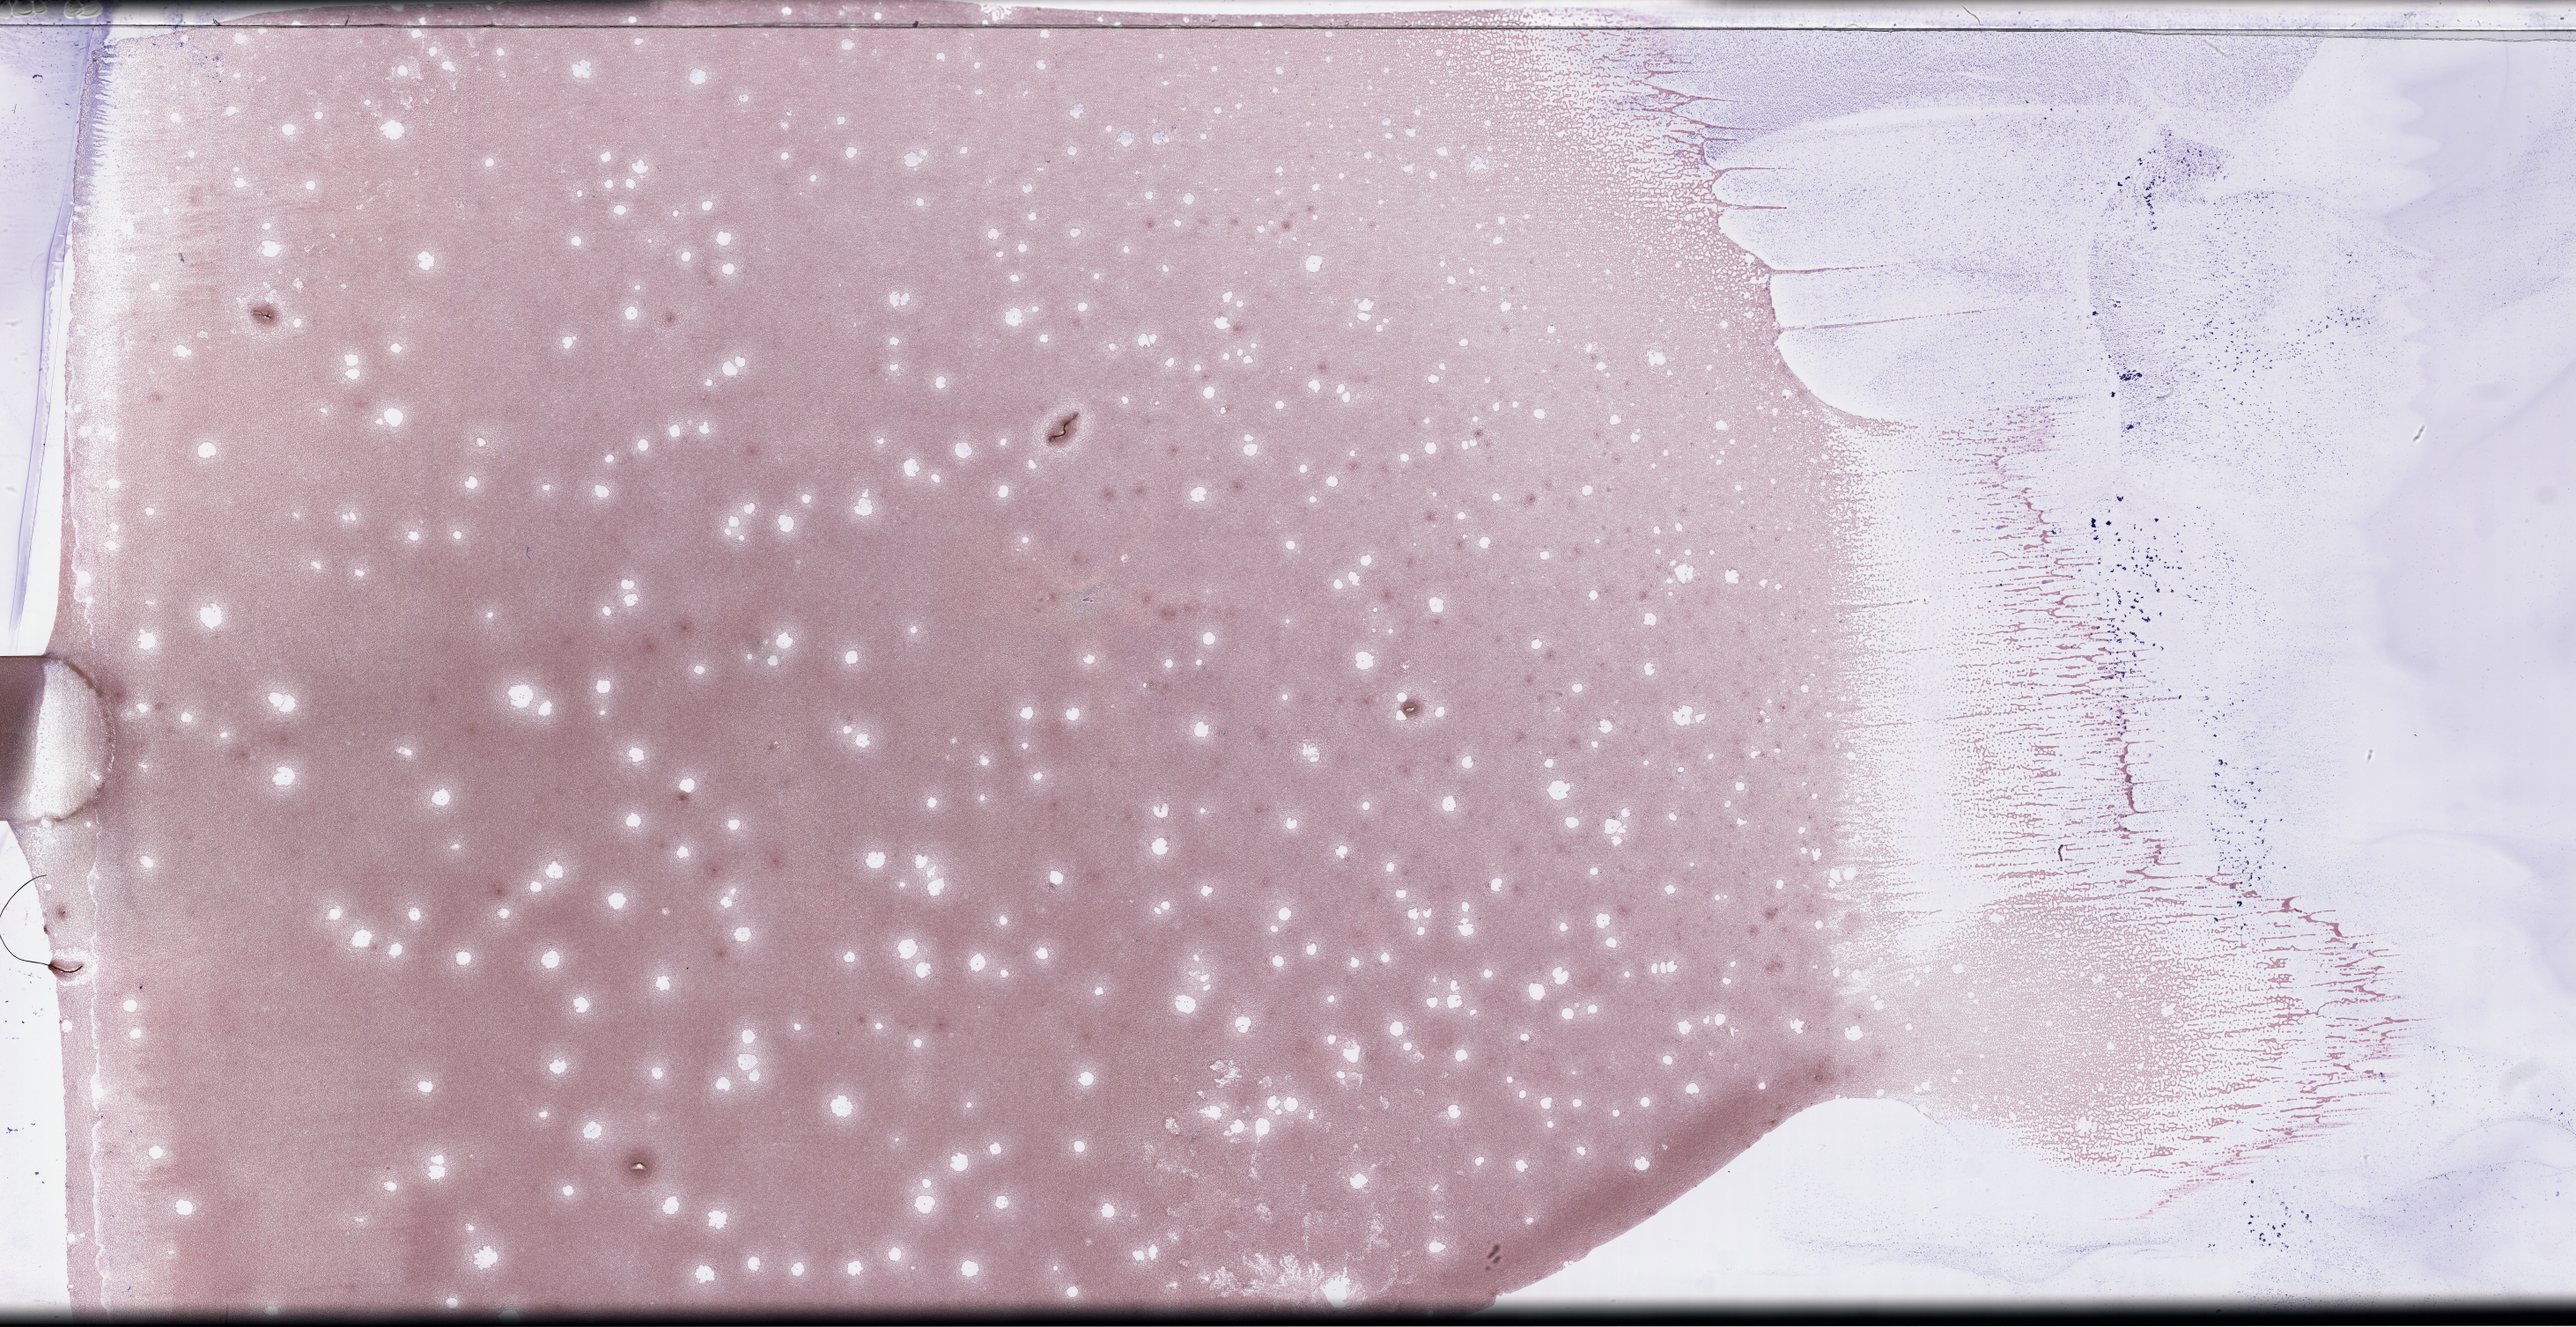
Wright-Giemsa-stained bone marrow smear, whole-slide image, low-resolution overview of the scanned area, about 47.2 x 24.3 mm. Male patient.
From a patient with: Plasma Cell Myeloma.